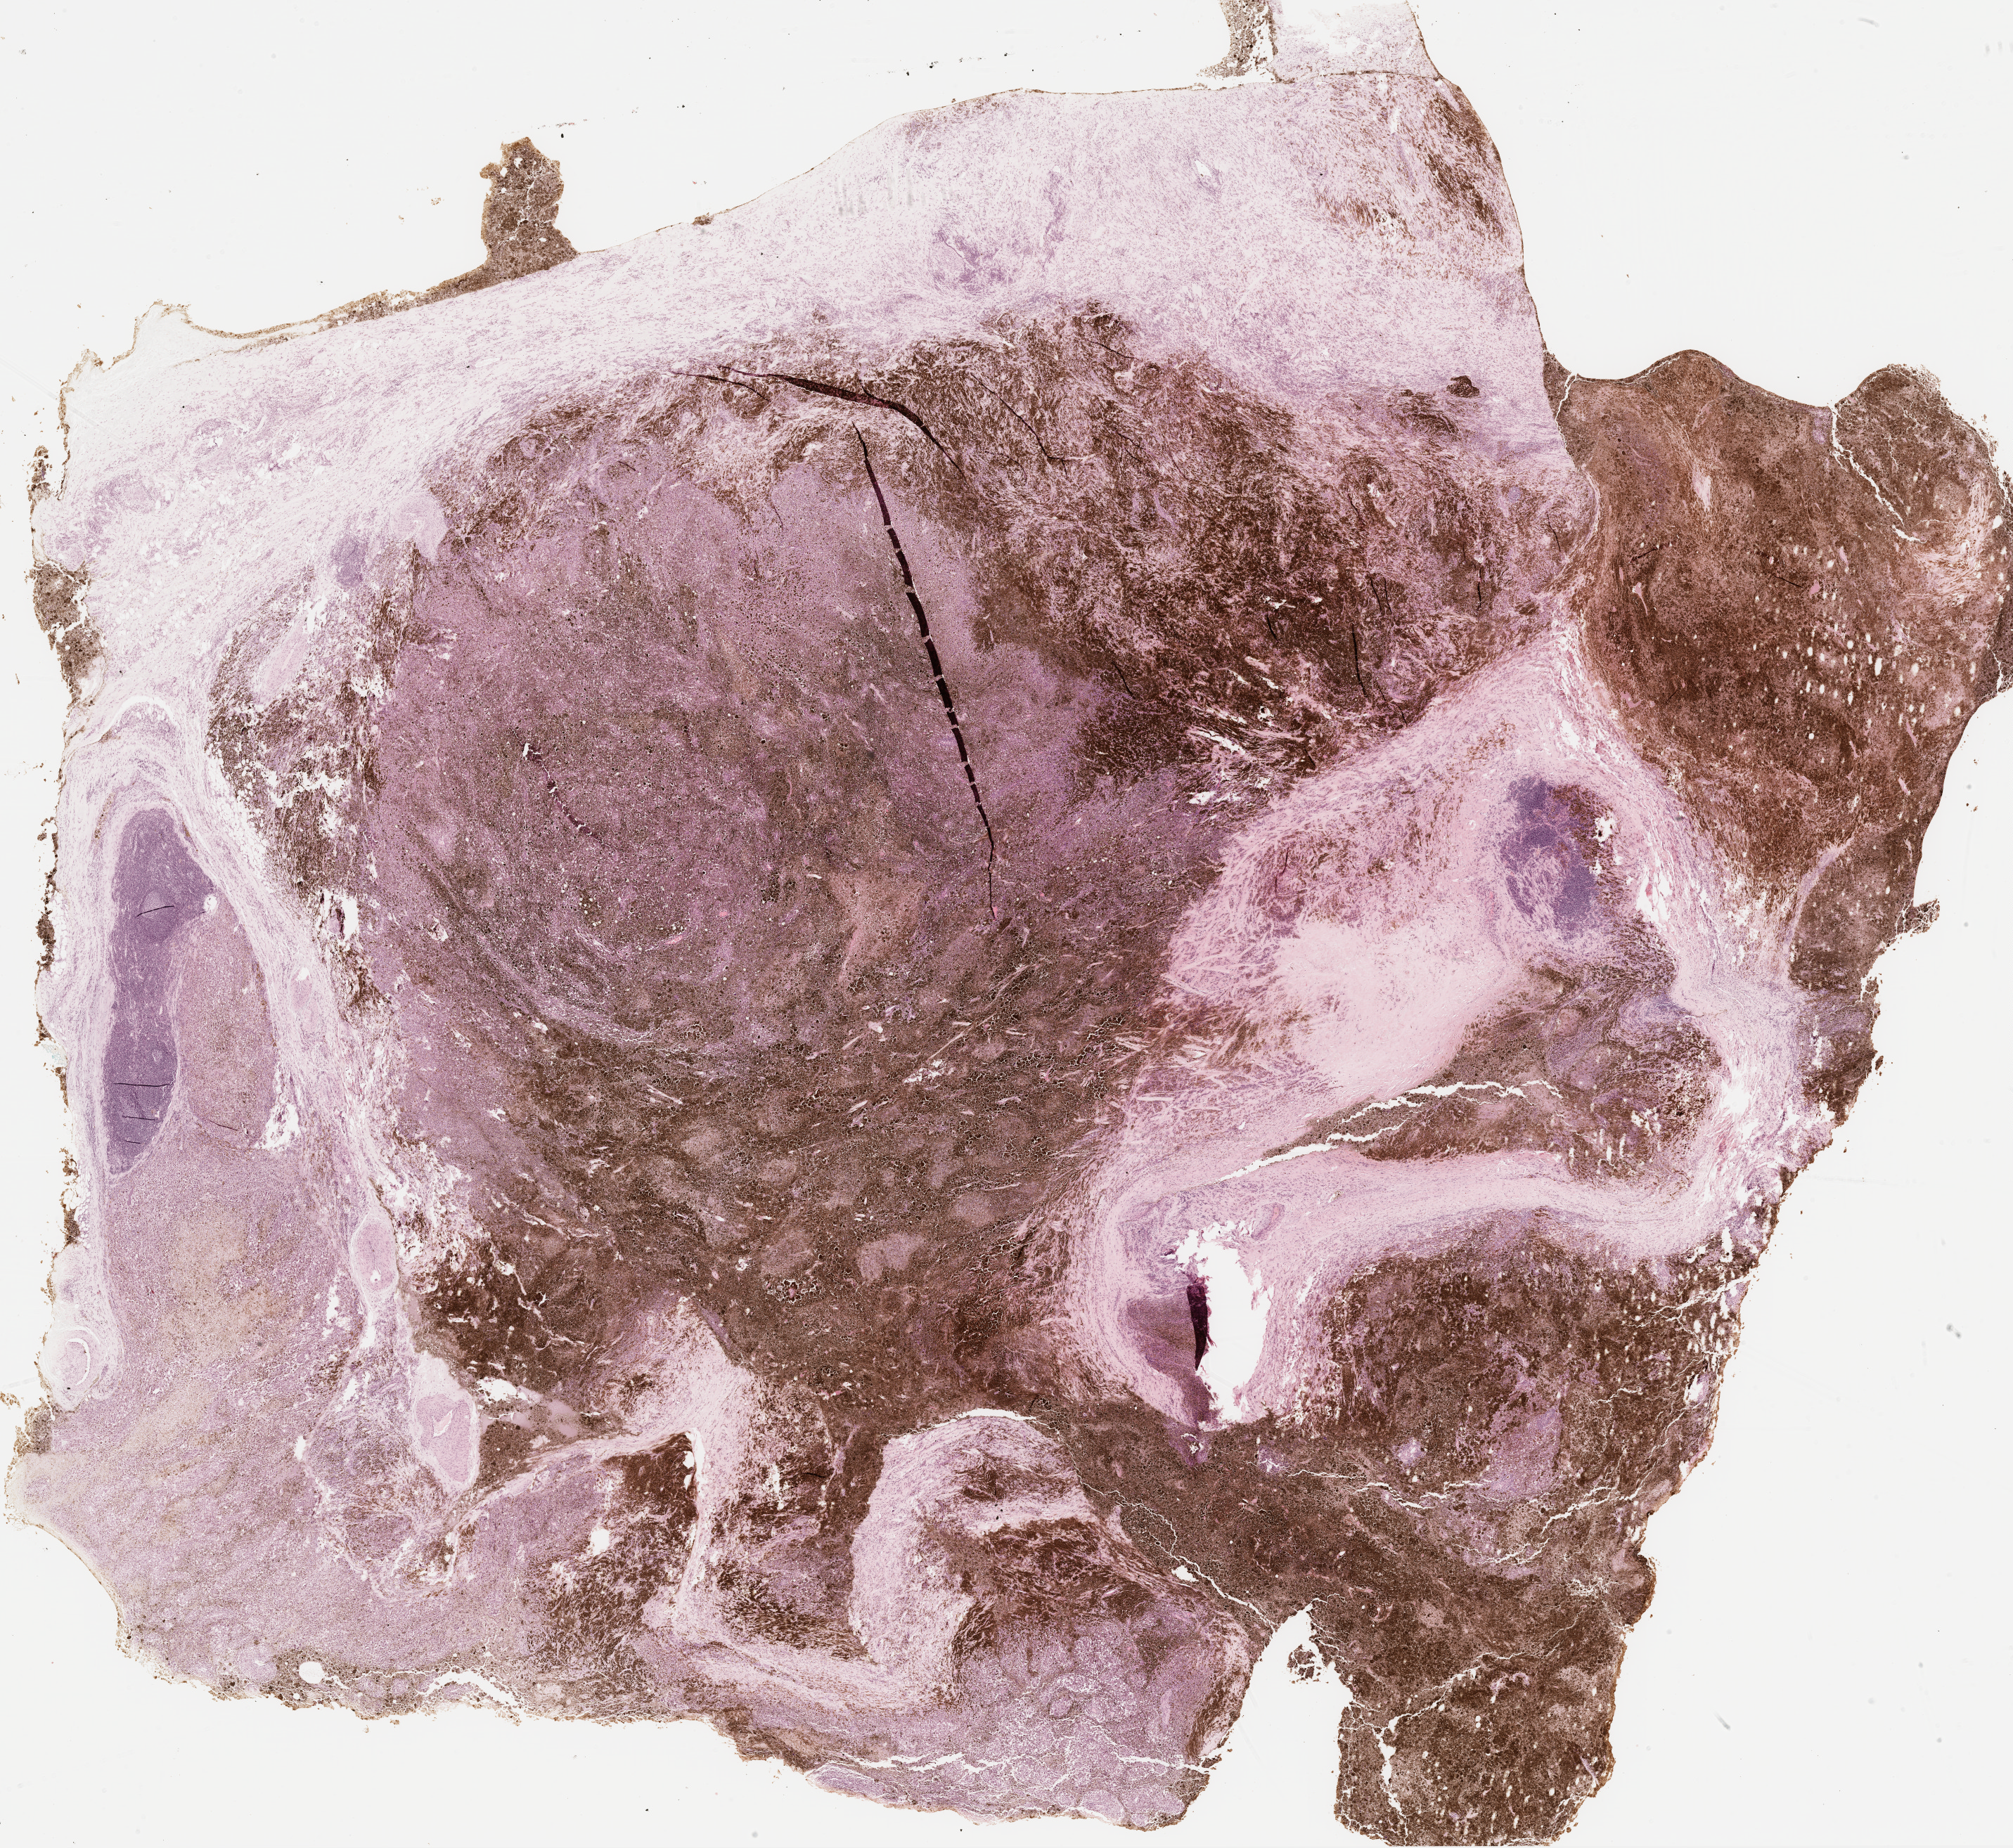
Hematoxylin and eosin (H&E) stained whole-slide image, shown as a low-resolution overview of the whole scanned area (about 23.1 x 21.2 mm, slide scanned at 20x); formalin-fixed paraffin-embedded (FFPE) diagnostic section; metastatic tumour sample, sampled site: lymph nodes of head, face and neck. Male patient; age at initial diagnosis 63 years.
This section: metastatic tumour tissue. Patient diagnosis: Malignant melanoma, NOS.